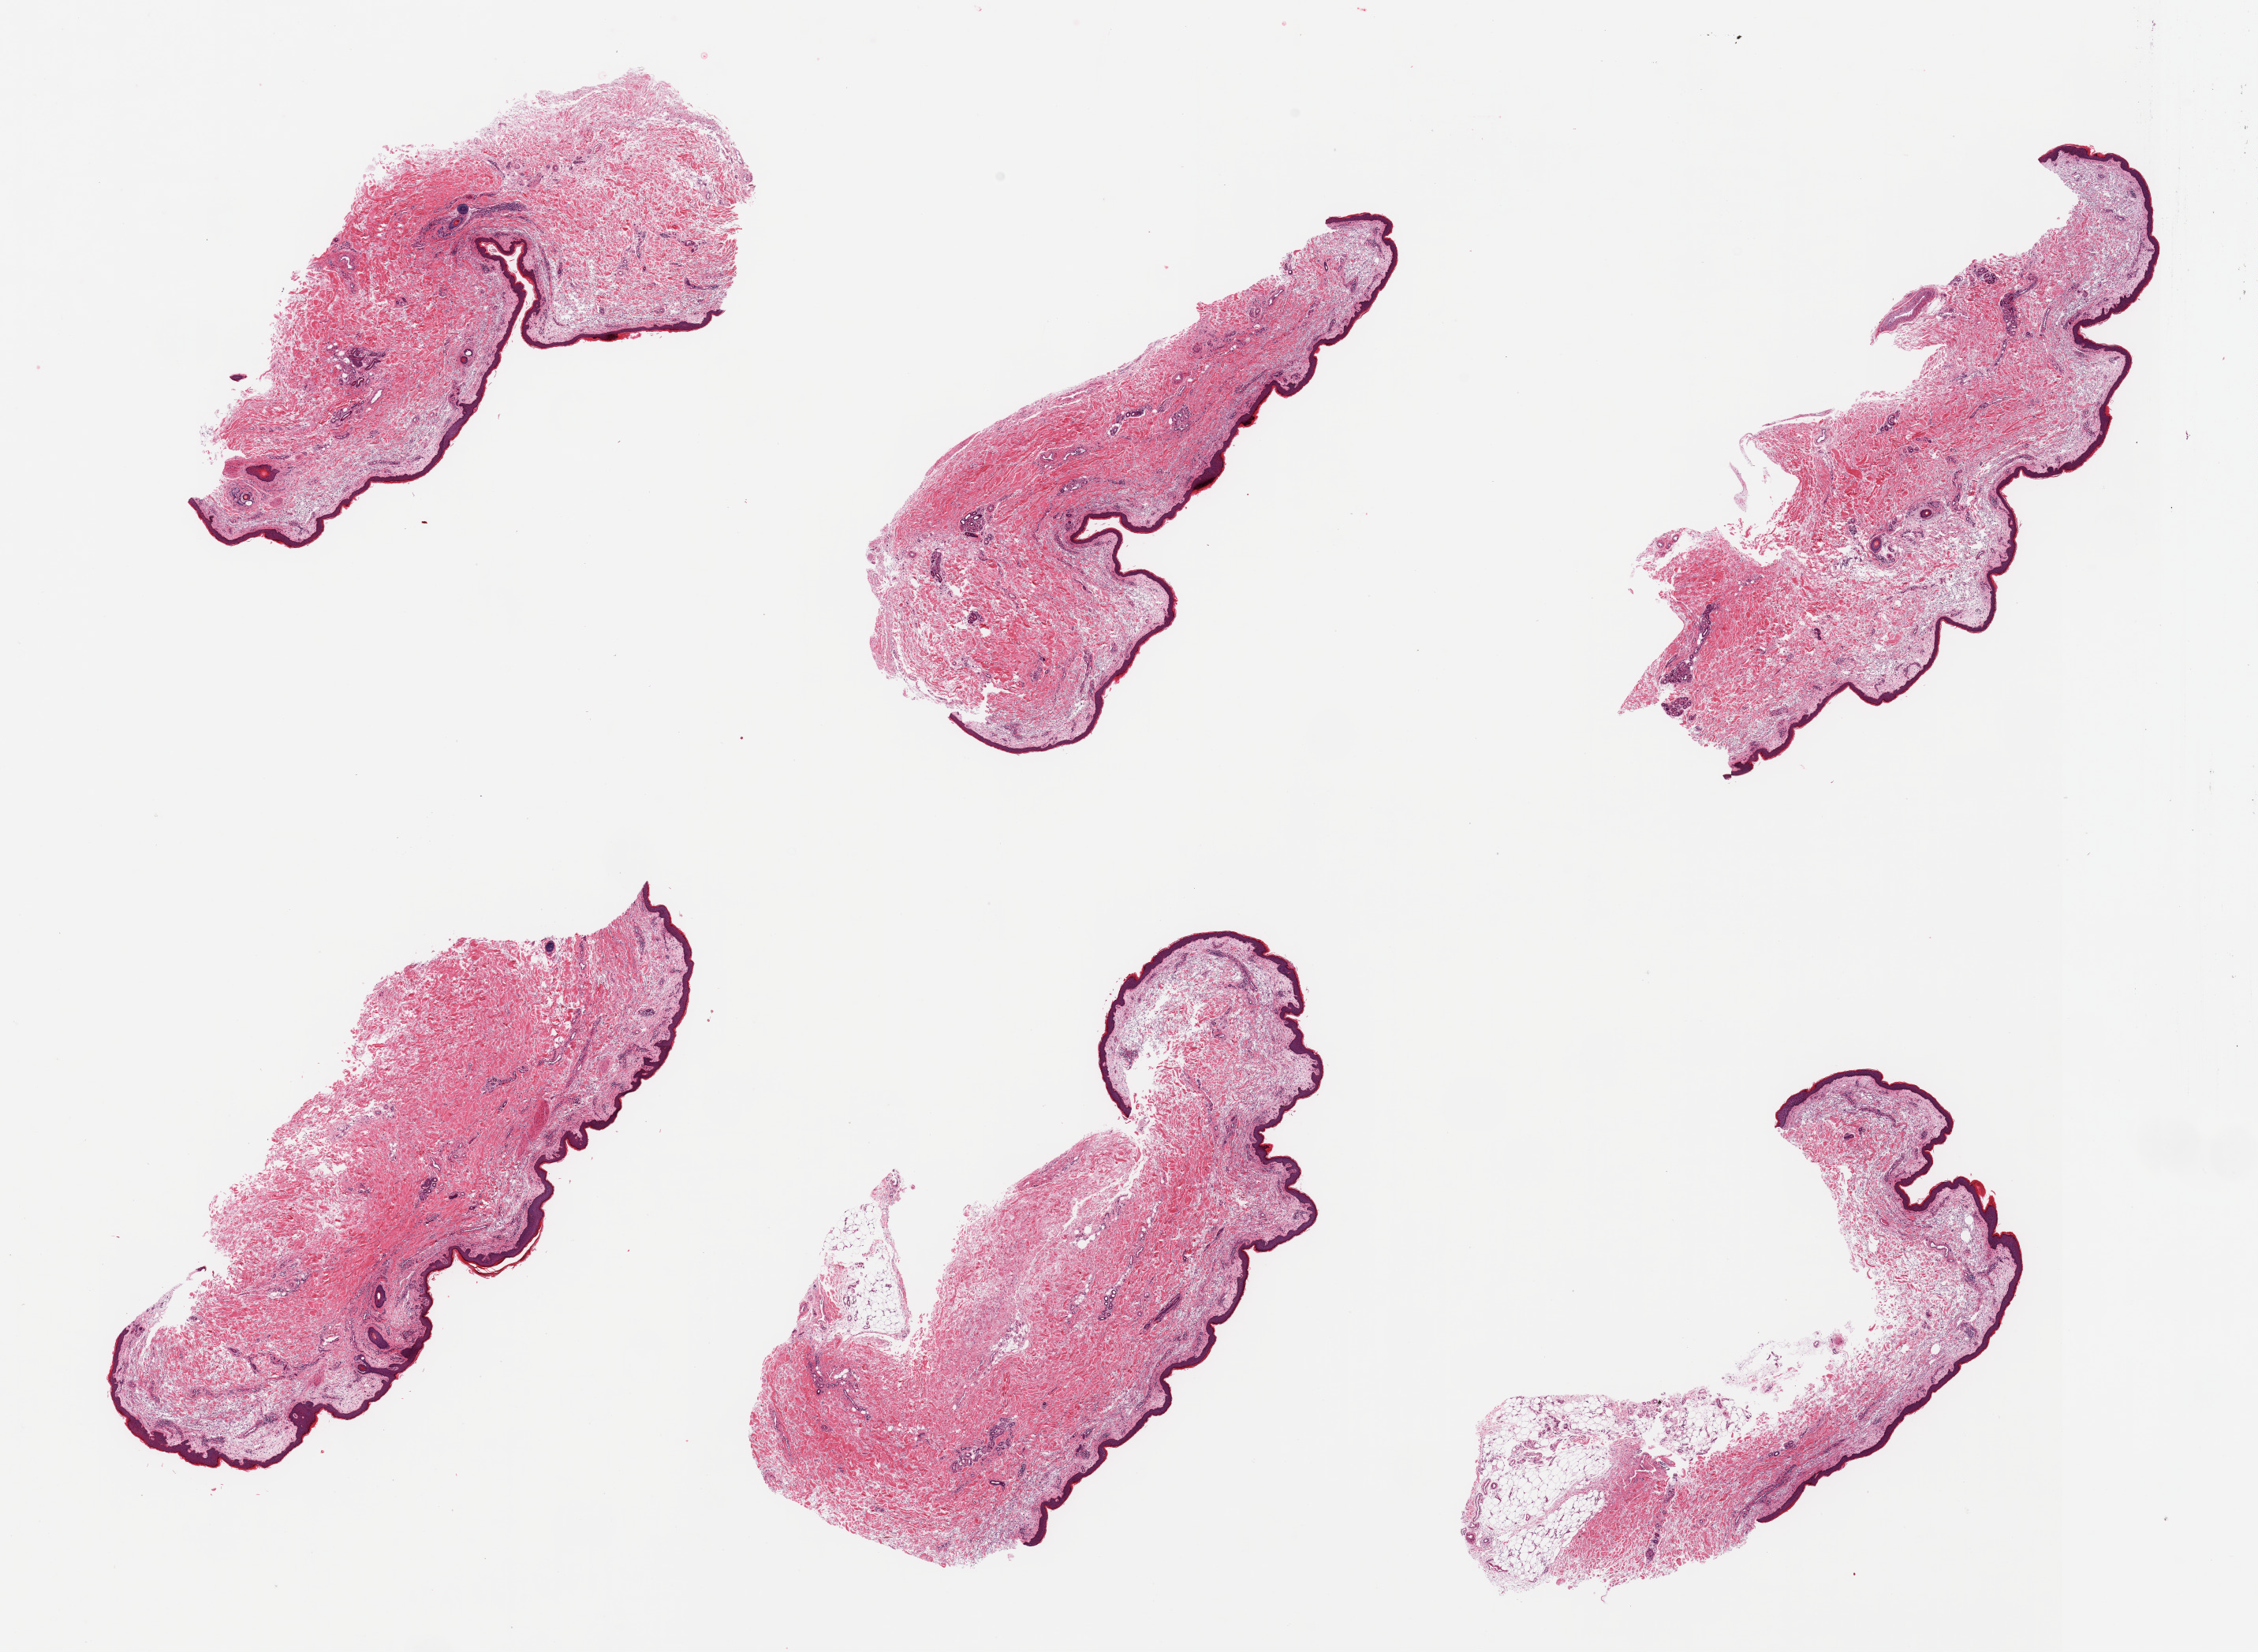
Haematoxylin and eosin whole-slide image, brightfield — whole scanned area (about 22.6 x 16.6 mm, from a 20x scan) shown as a low-resolution overview; PAXgene-fixed paraffin-embedded (PFPE) section; section of skin of lower leg (target tissue); tissue donor sample. Male donor.
- reviewer comment on this tissue sample: 6 pieces, no significant dermal fat; mild dermal solar elastosis. Squamous epithlium is ~50-55 microns